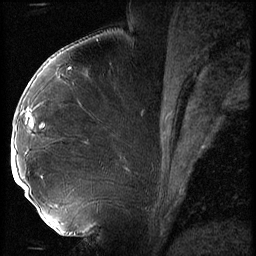
Breast MRI (dynamic contrast-enhanced), one sagittal slice; position 31 of 56 along the scan axis; 3 images stored at this slice position (order not interpretable as contrast timing); 1.5 T; TE 4.2 ms, TR 9 ms; 256 × 256 image matrix, field of view 180 × 180 mm. Patient: female, 43 years. From the clinical record (not read from this slice): setting: breast cancer imaged before/during neoadjuvant chemotherapy; receptor status: HER2-positive.
Annotated regions visible in this slice (semi-automatically segmented with operator editing):
- analysis volume of interest (the breast-tissue region the enhancement analysis was run in; not a lesion): bounding box (x1, y1, x2, y2) in pixels: (12, 92, 74, 211)
- tumour enhancement mask (voxels above the 140 % enhancement threshold inside the analysis volume of interest): (12, 116, 29, 191)